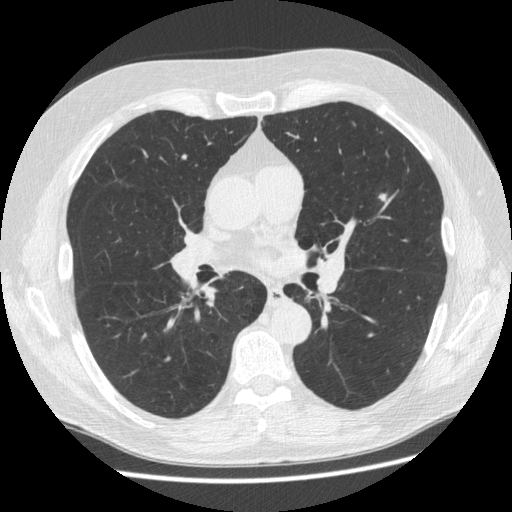
Low-dose screening chest CT, one axial slice. Slice 301 of 545 in the series (ordered by position). Reconstruction kernel STANDARD. Lung window (W 1500 / L -600 HU). 1.25 mm slice thickness. 512 × 512 image matrix, field of view 360 × 360 mm.
Outlined on this slice (outlined manually by an expert reader):
- lesion 1 (nodule, upper lobe of left lung): bounding box (x1, y1, x2, y2) in pixels: (379, 194, 386, 201)